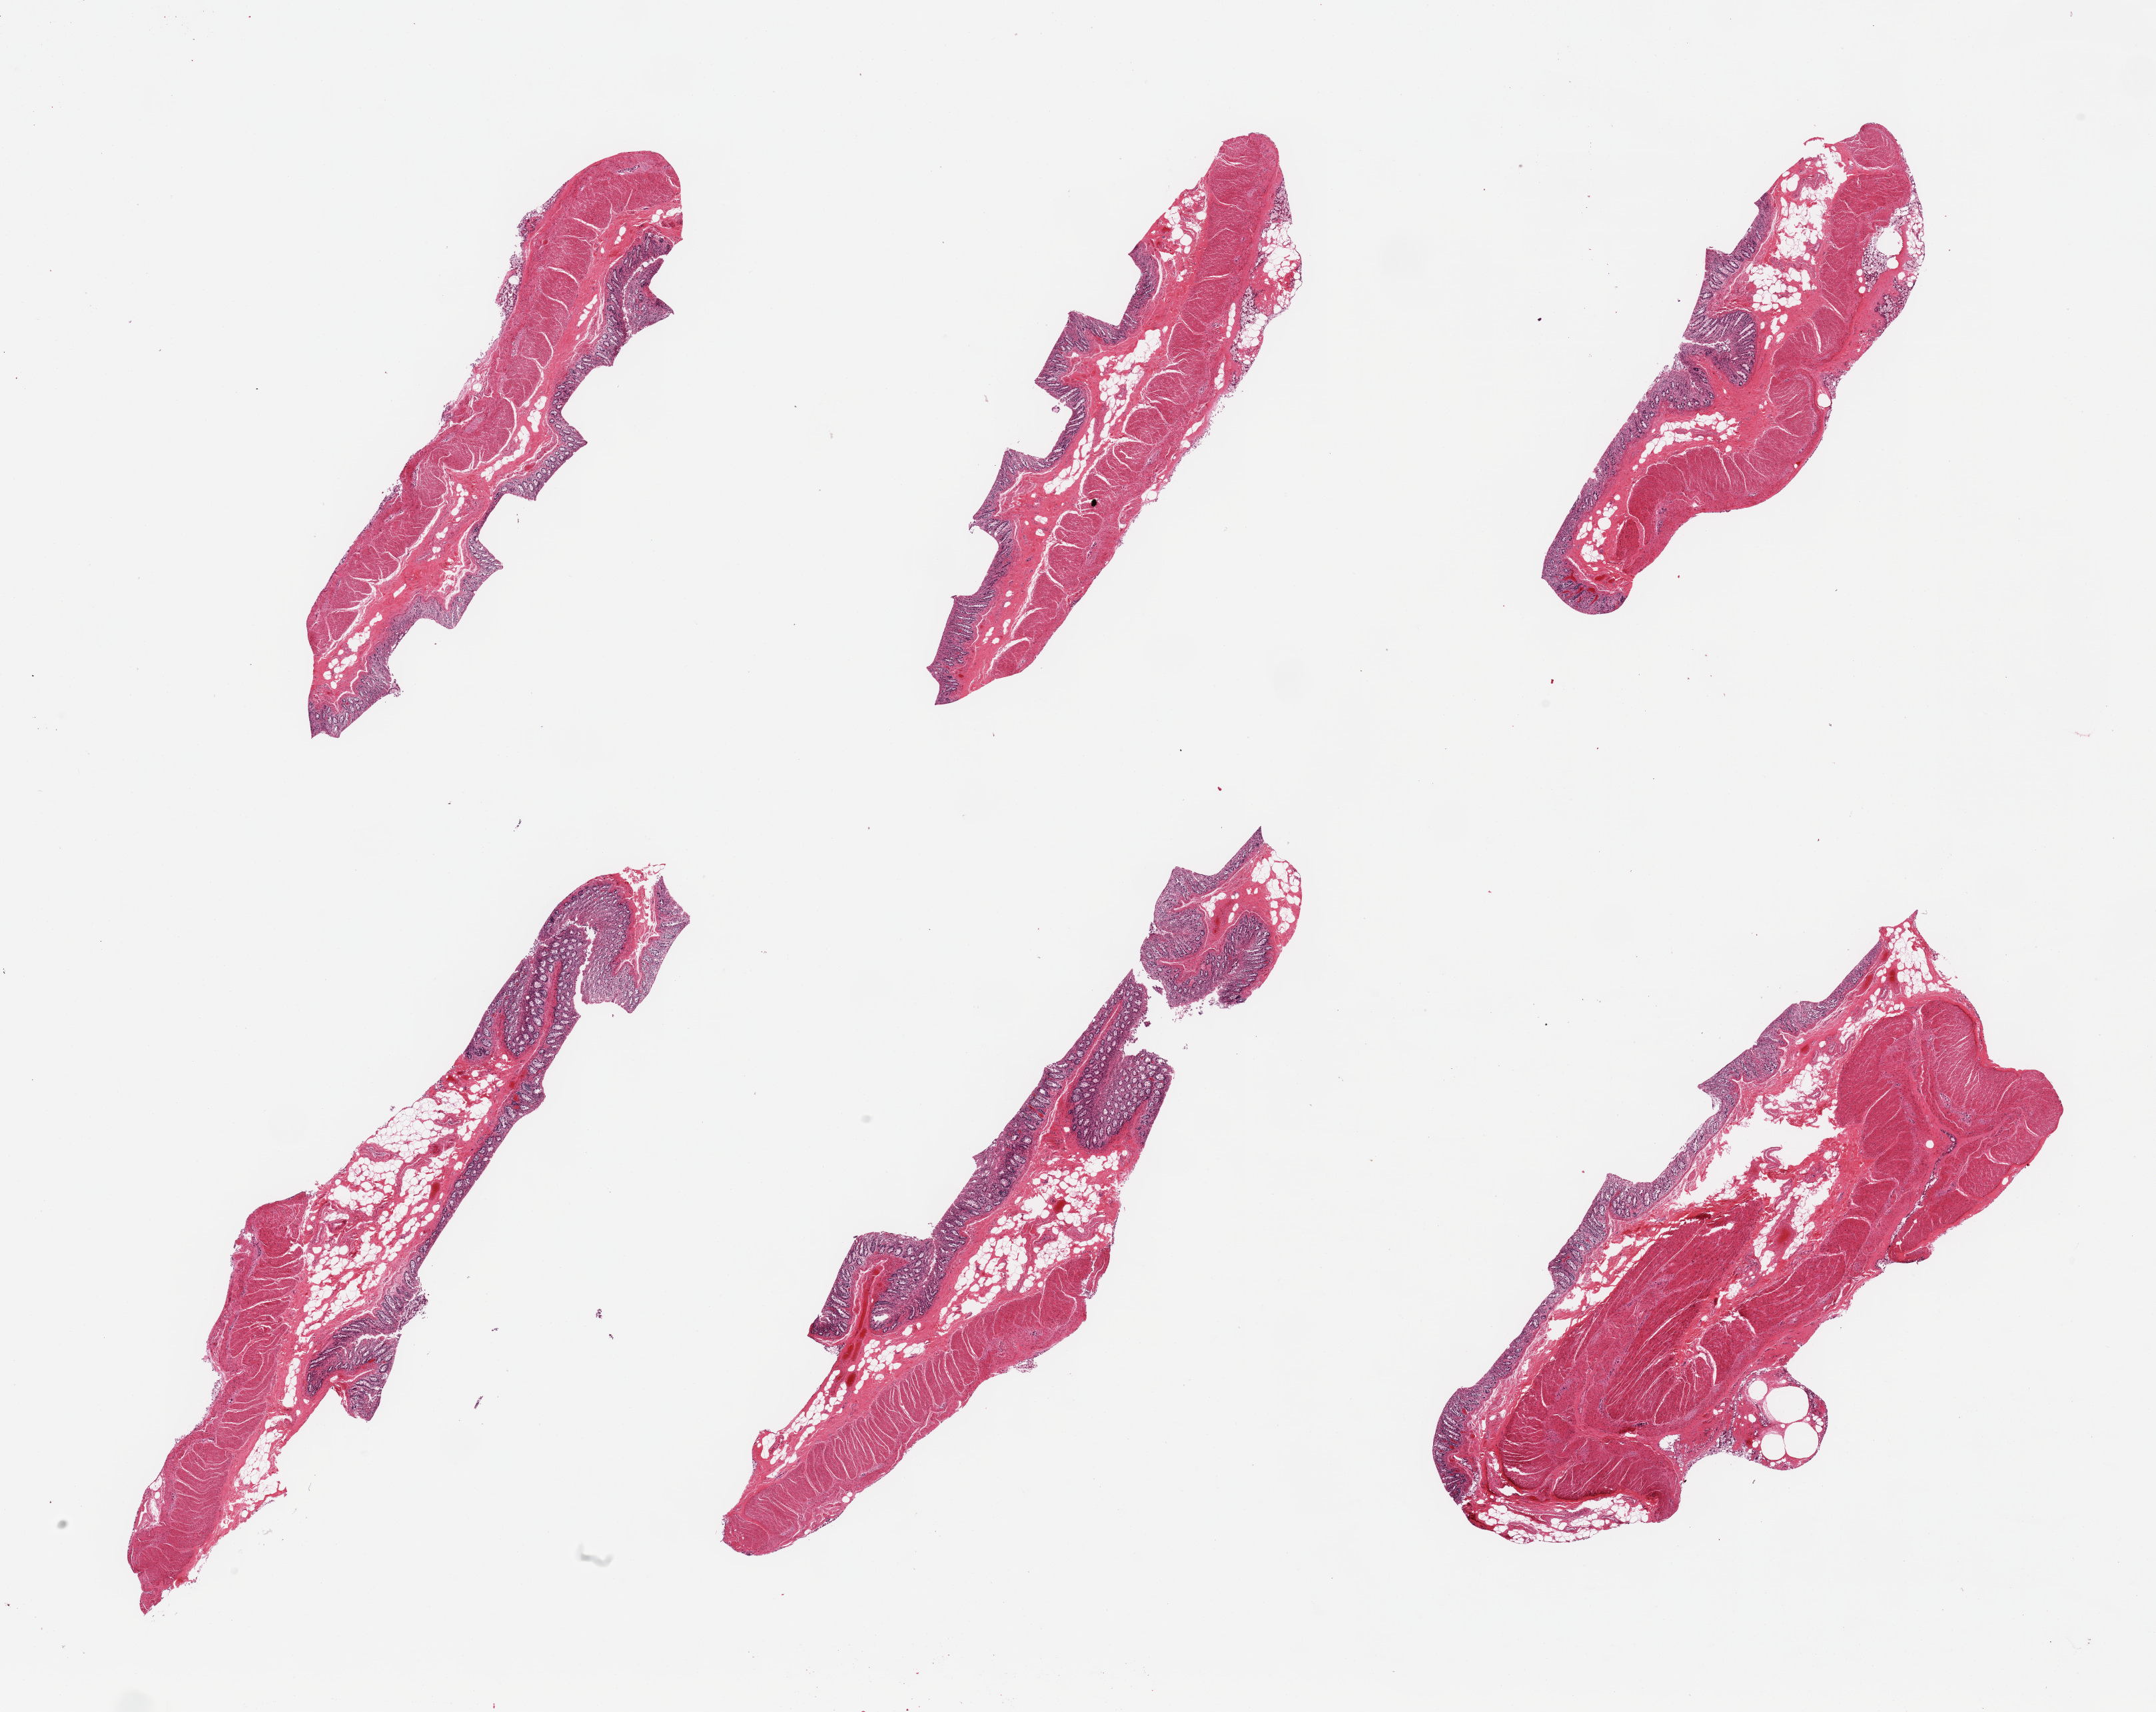
H&E whole-slide image, a low-resolution overview of the entire scanned area, about 25.6 x 20.3 mm; PAXgene-fixed, paraffin-embedded tissue; section of transverse colon (target tissue); donor tissue sample. Male donor.
- review note (as recorded): 6 pieces, target mucosa up to 0.4mm, ~10% of thickness, moderately advanced autolysis